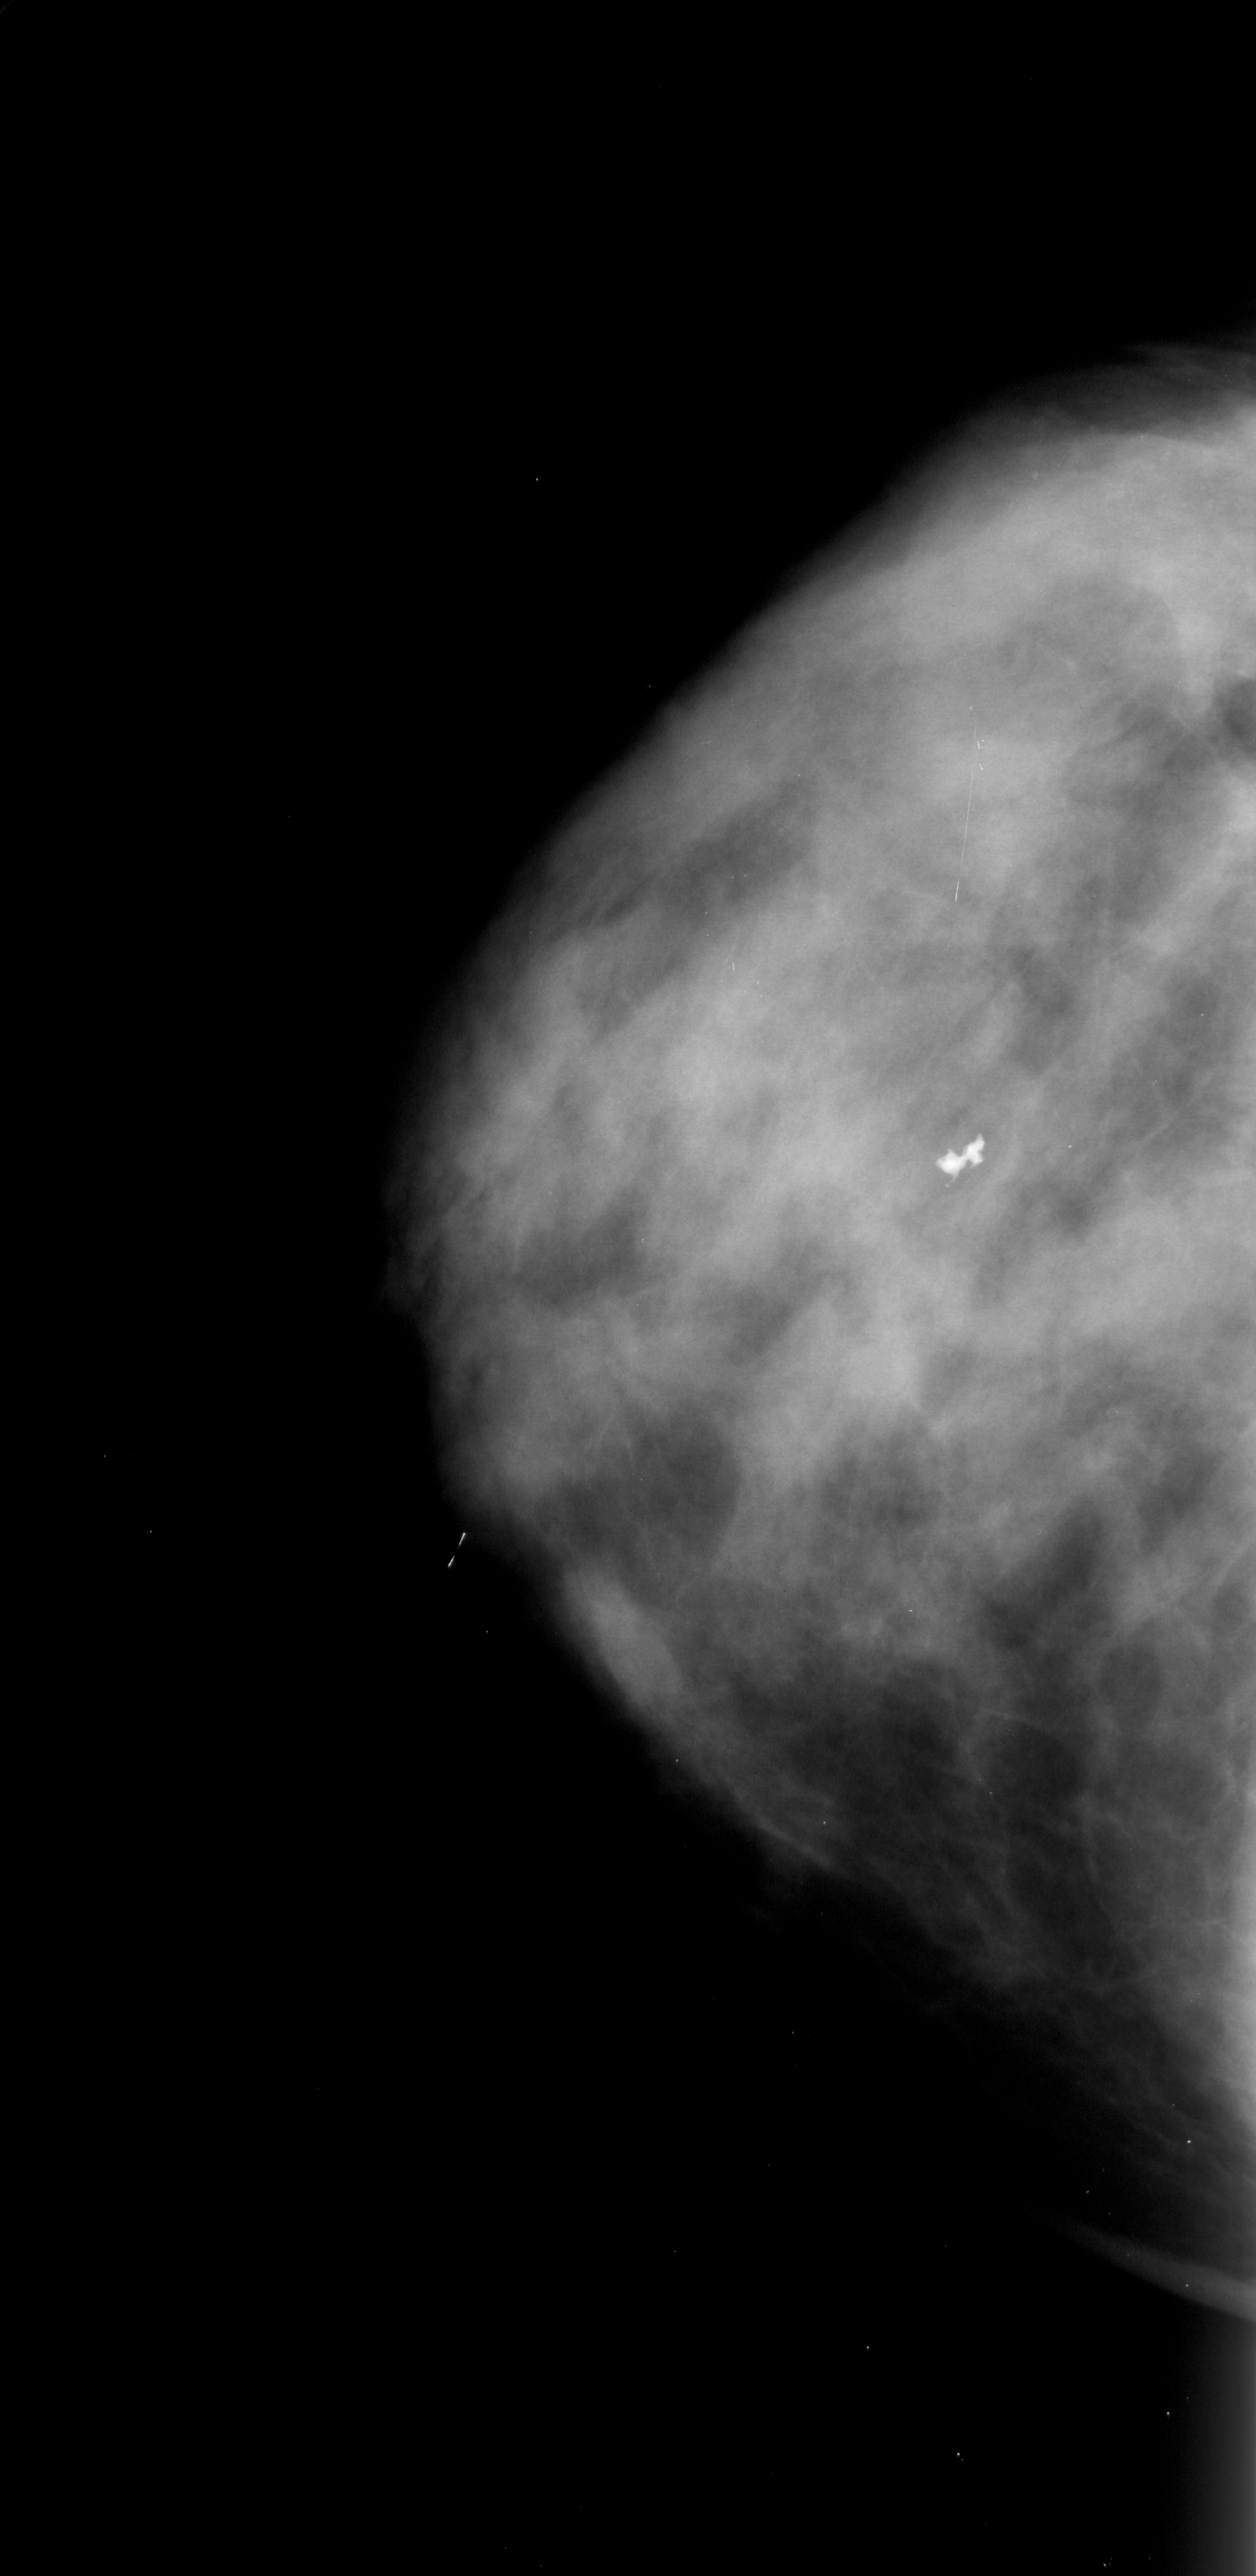
Scanned film-screen mammogram; left breast; craniocaudal (CC) view; 1256 × 2576 image matrix.
Marked abnormalities (boxes around the expert regions of interest):
- calcifications, morphology pleomorphic, distribution clustered; BI-RADS assessment category 4; pathology result (as recorded, not read from the image): malignant: bounding box <983,407,1196,554> (left, top, right, bottom; pixels)